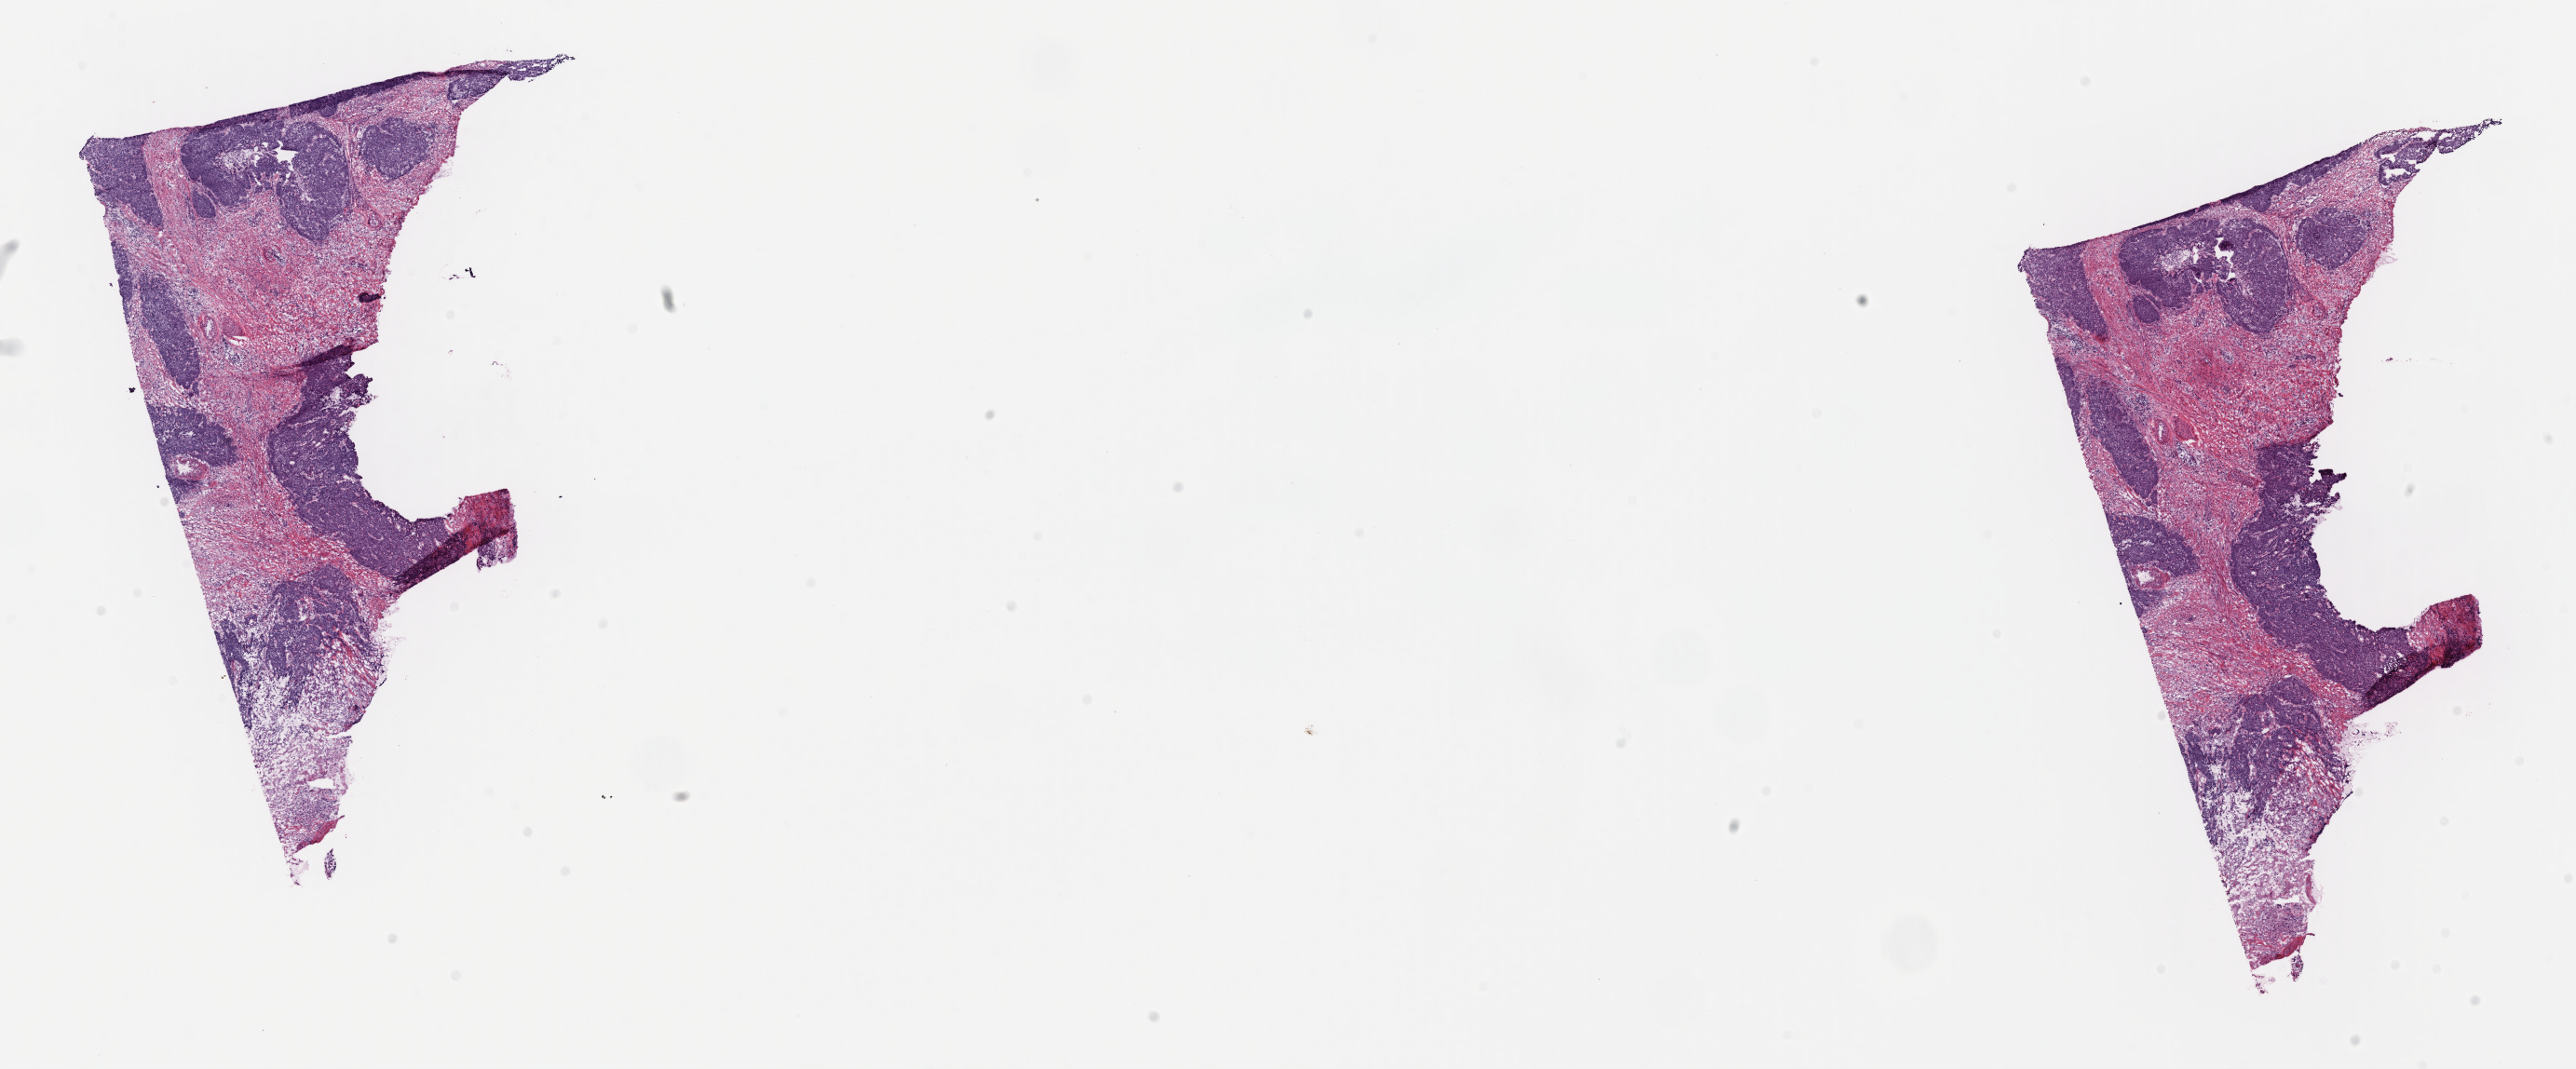
Digitized Hematoxylin and eosin (H&E) stained tissue section (whole slide) — shown as a low-resolution overview of the whole scanned area (about 21.9 x 9.1 mm, acquisition: 40x scan), frozen section, cervix, primary tumour sample. Patient: female, age at initial diagnosis 58 years. Histologic grade: G3 (poorly differentiated). Slide review estimates, as recorded: tumour cells 40%, tumour nuclei 65%, normal cells 50%, stromal cells 7%, necrosis 3%. Infiltration values recorded for this section: lymphocyte infiltration 10%, monocyte infiltration 0%, neutrophil infiltration 0%.
• FIGO stage: IB1
• histologic diagnosis: Squamous cell carcinoma, large cell, nonkeratinizing, NOS (cervix uteri)